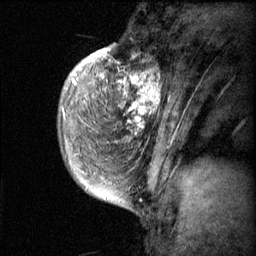
Breast MRI (dynamic contrast-enhanced), one sagittal slice; slice 14 of 60 in the series (ordered by position); dynamic contrast-enhanced series, image 2 of 3 at this slice position (ordered by acquisition); 1.5 T; TE 4.2 ms, TR 11.1 ms; 2 mm slice thickness; 256 × 256 image matrix. Female patient, age 50 years.
Structures marked on this image (semi-automatic segmentation, software-assisted and operator-edited):
- analysis volume of interest (the breast-tissue region the enhancement analysis was run in; not a lesion): bounding box <82,56,168,143> (left, top, right, bottom; pixels)
- tumour enhancement mask (voxels above the 70 % enhancement threshold inside the analysis volume of interest): <82,56,163,143>